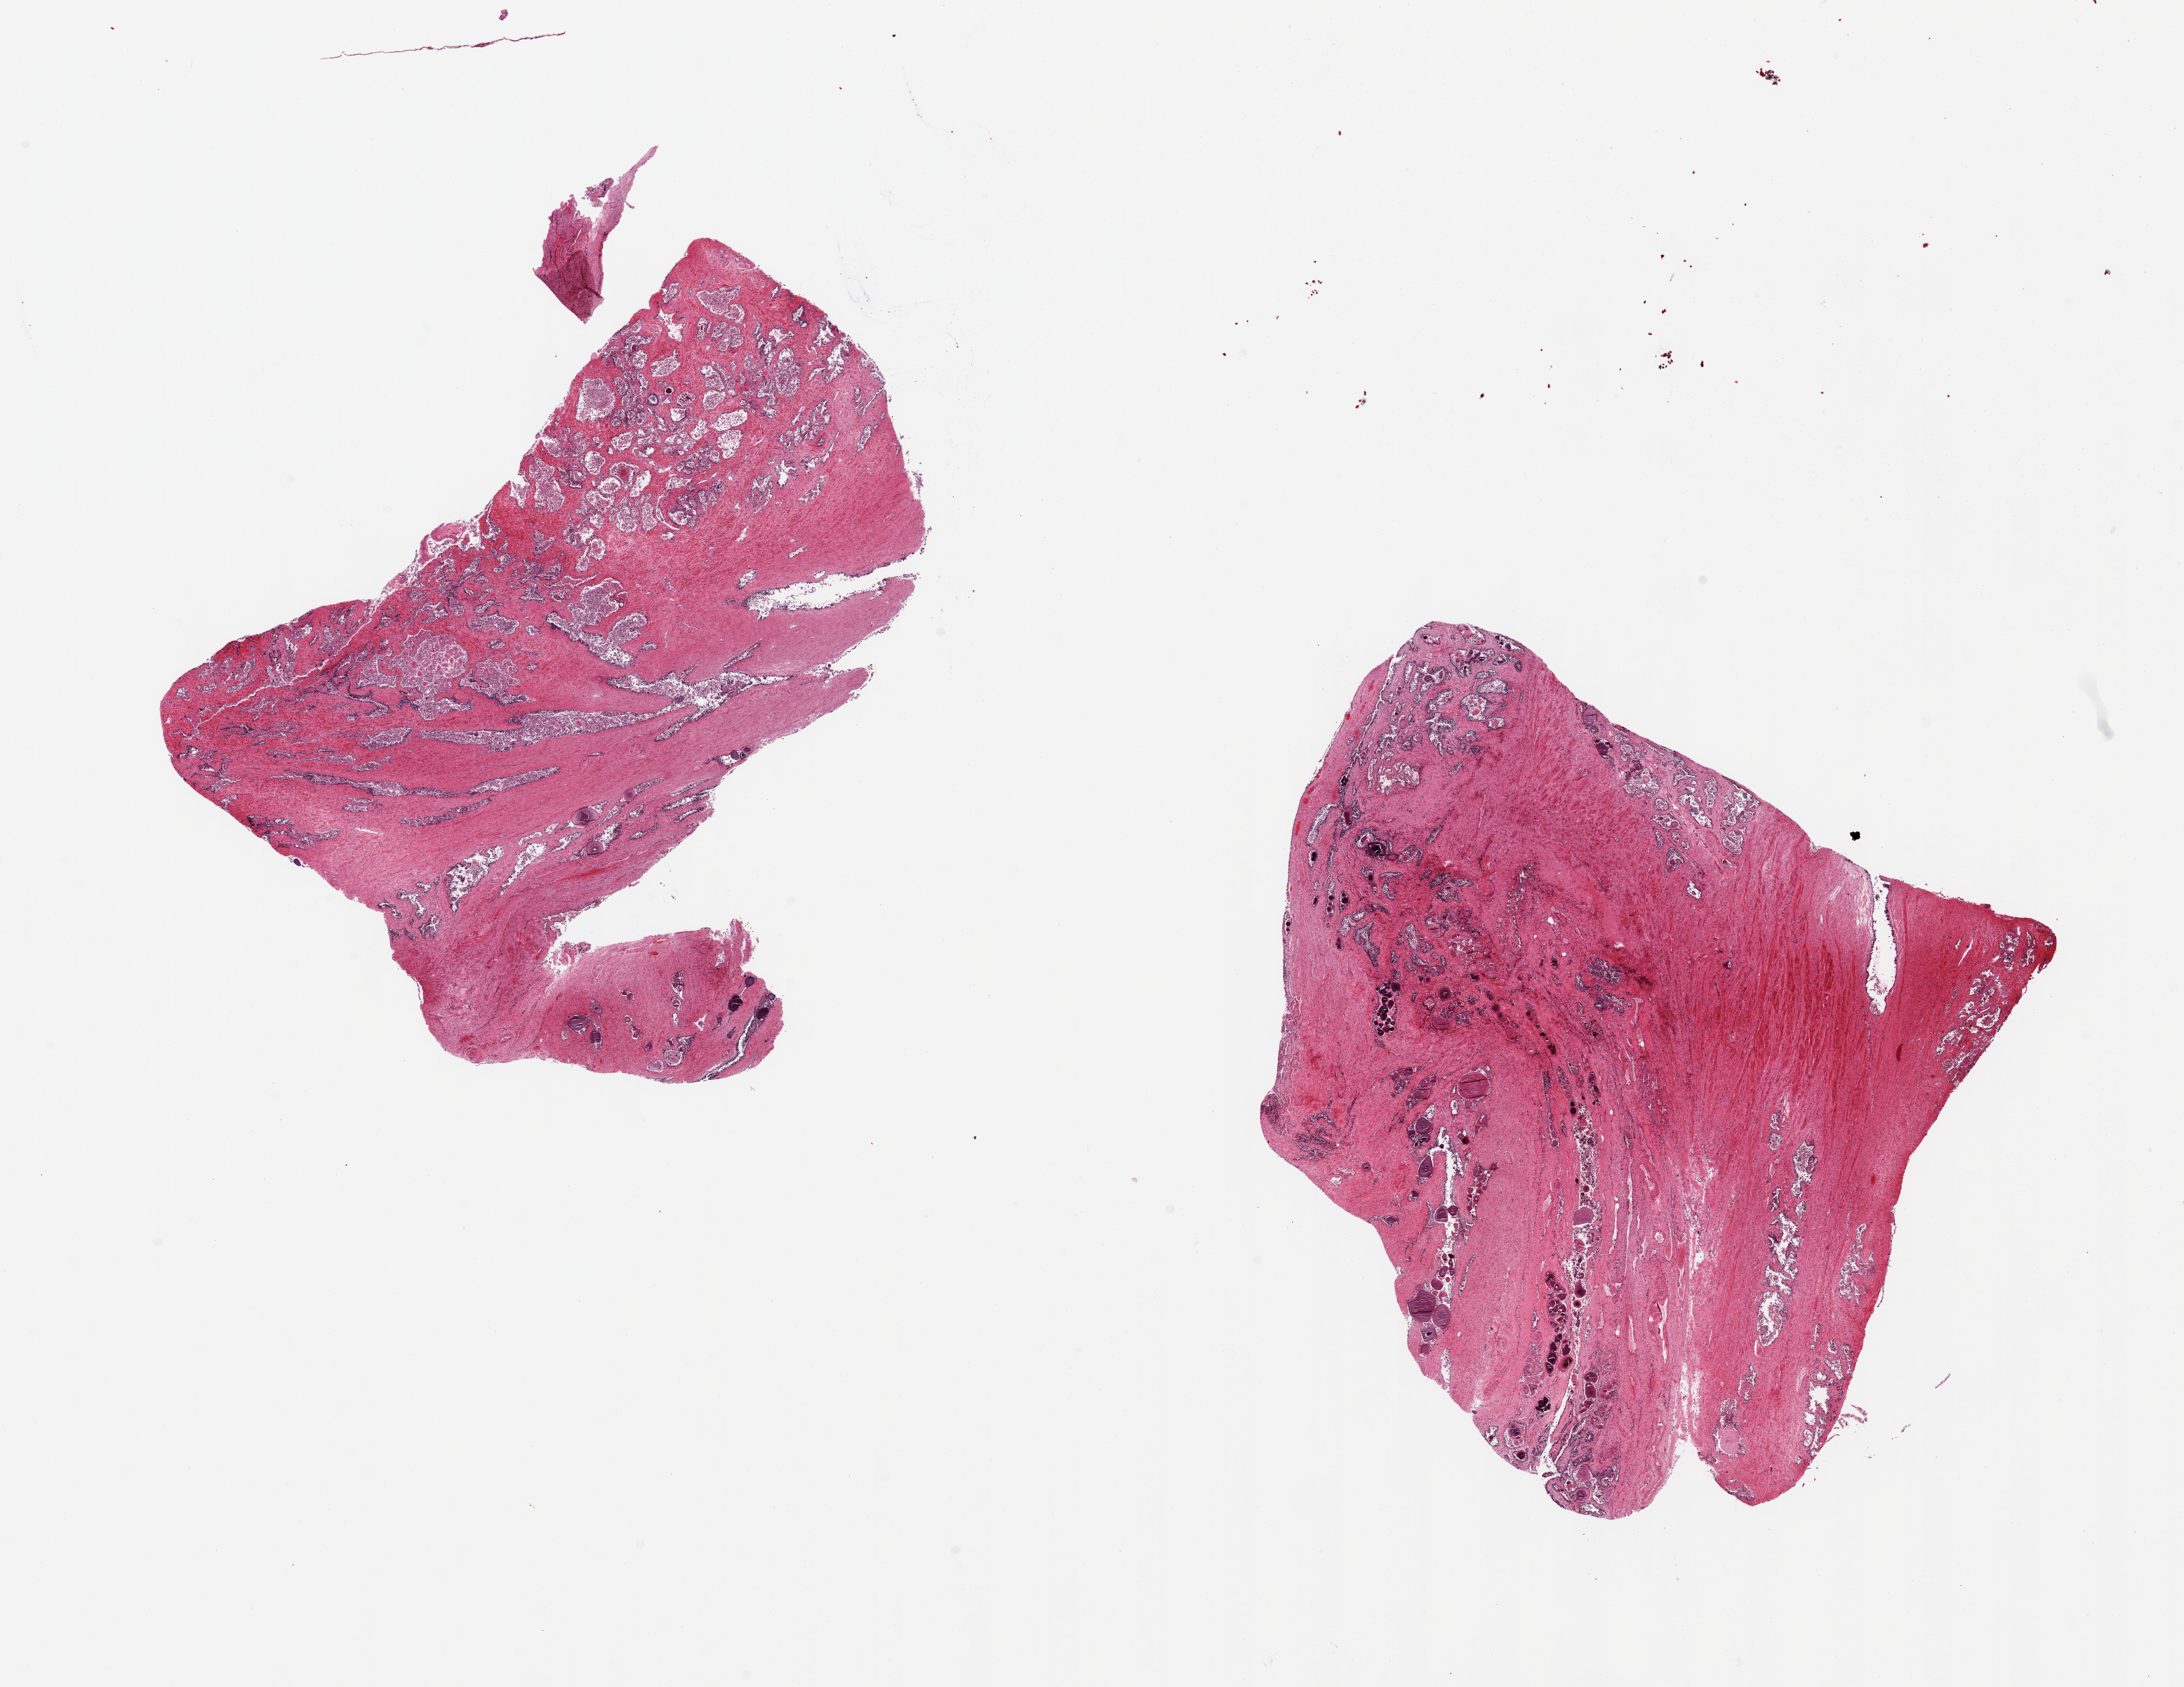
Haematoxylin and eosin whole-slide image, a low-resolution overview of the entire scanned area, about 24.6 x 19.0 mm (from a 20x scan). PAXgene-fixed paraffin-embedded (PFPE) section. Section of prostate (target tissue). Tissue donor sample. Donor: male.
• review note (as recorded): 2 pieces ~8x7mm, glands totally autolyzed